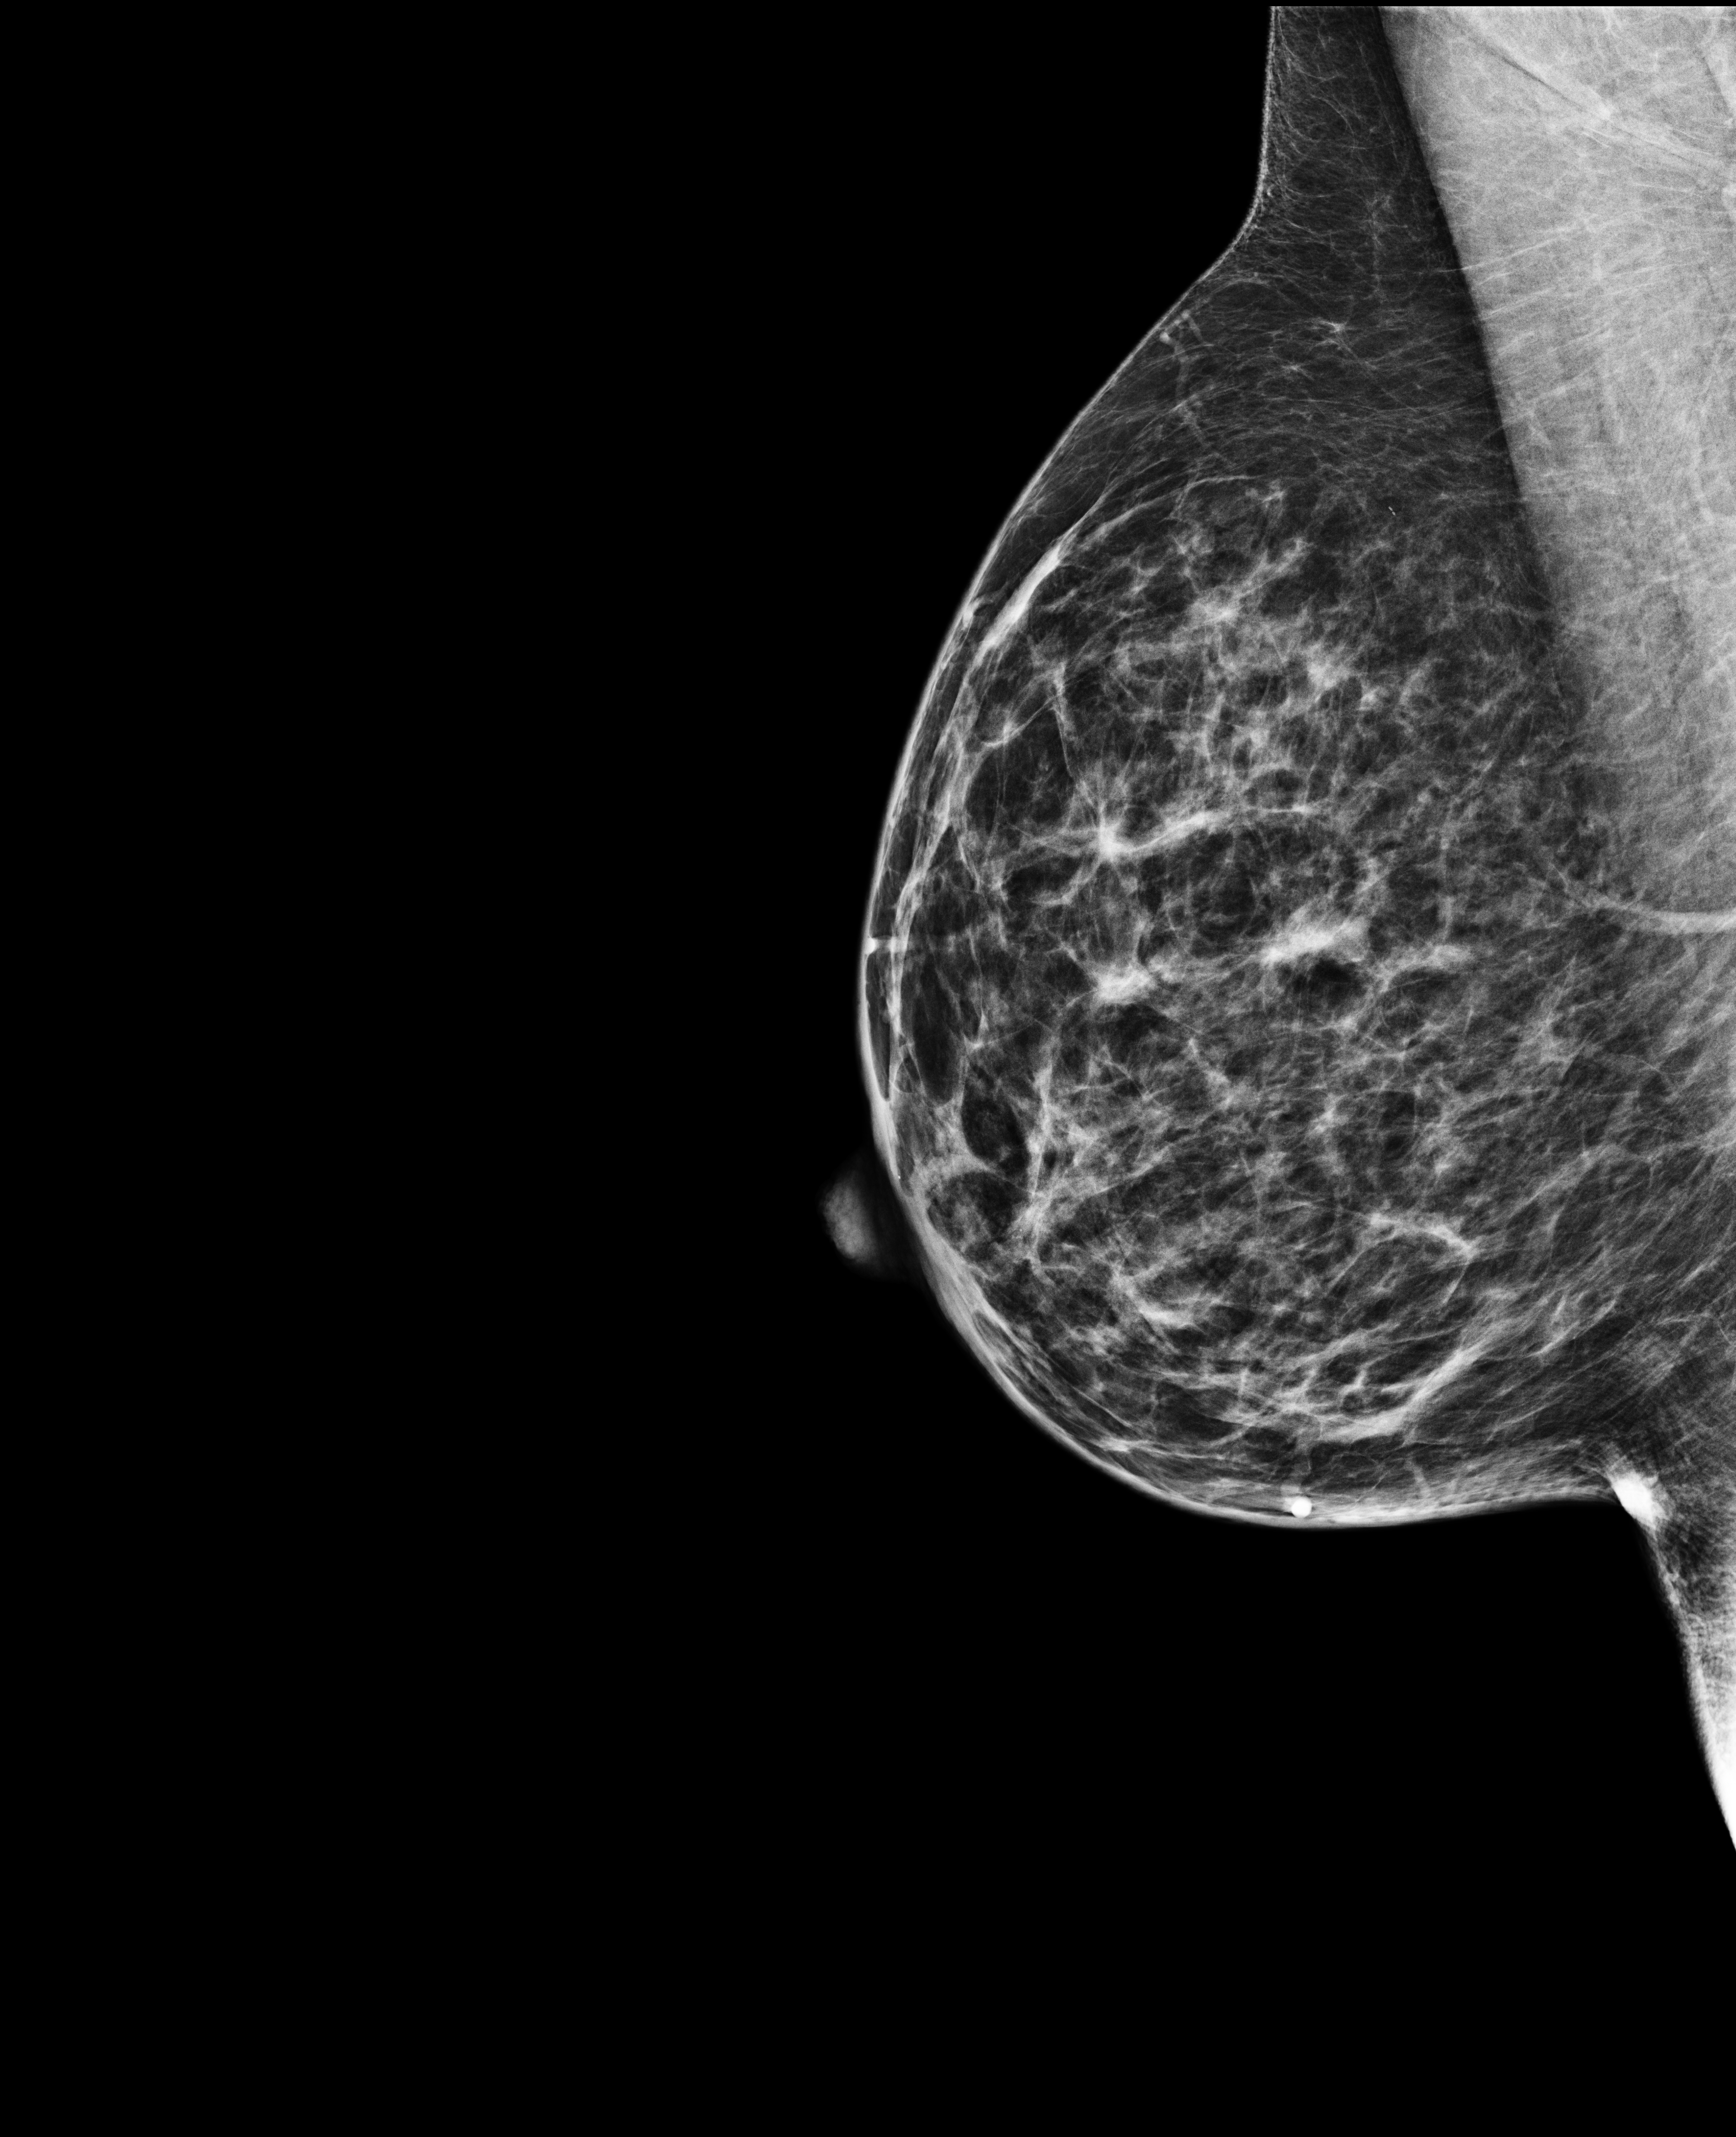
Screening examination; system: Selenia Dimensions. Patient: female, 49 years.
Image type: full-field digital mammogram. Breast: right. Projection: medio-lateral oblique projection.